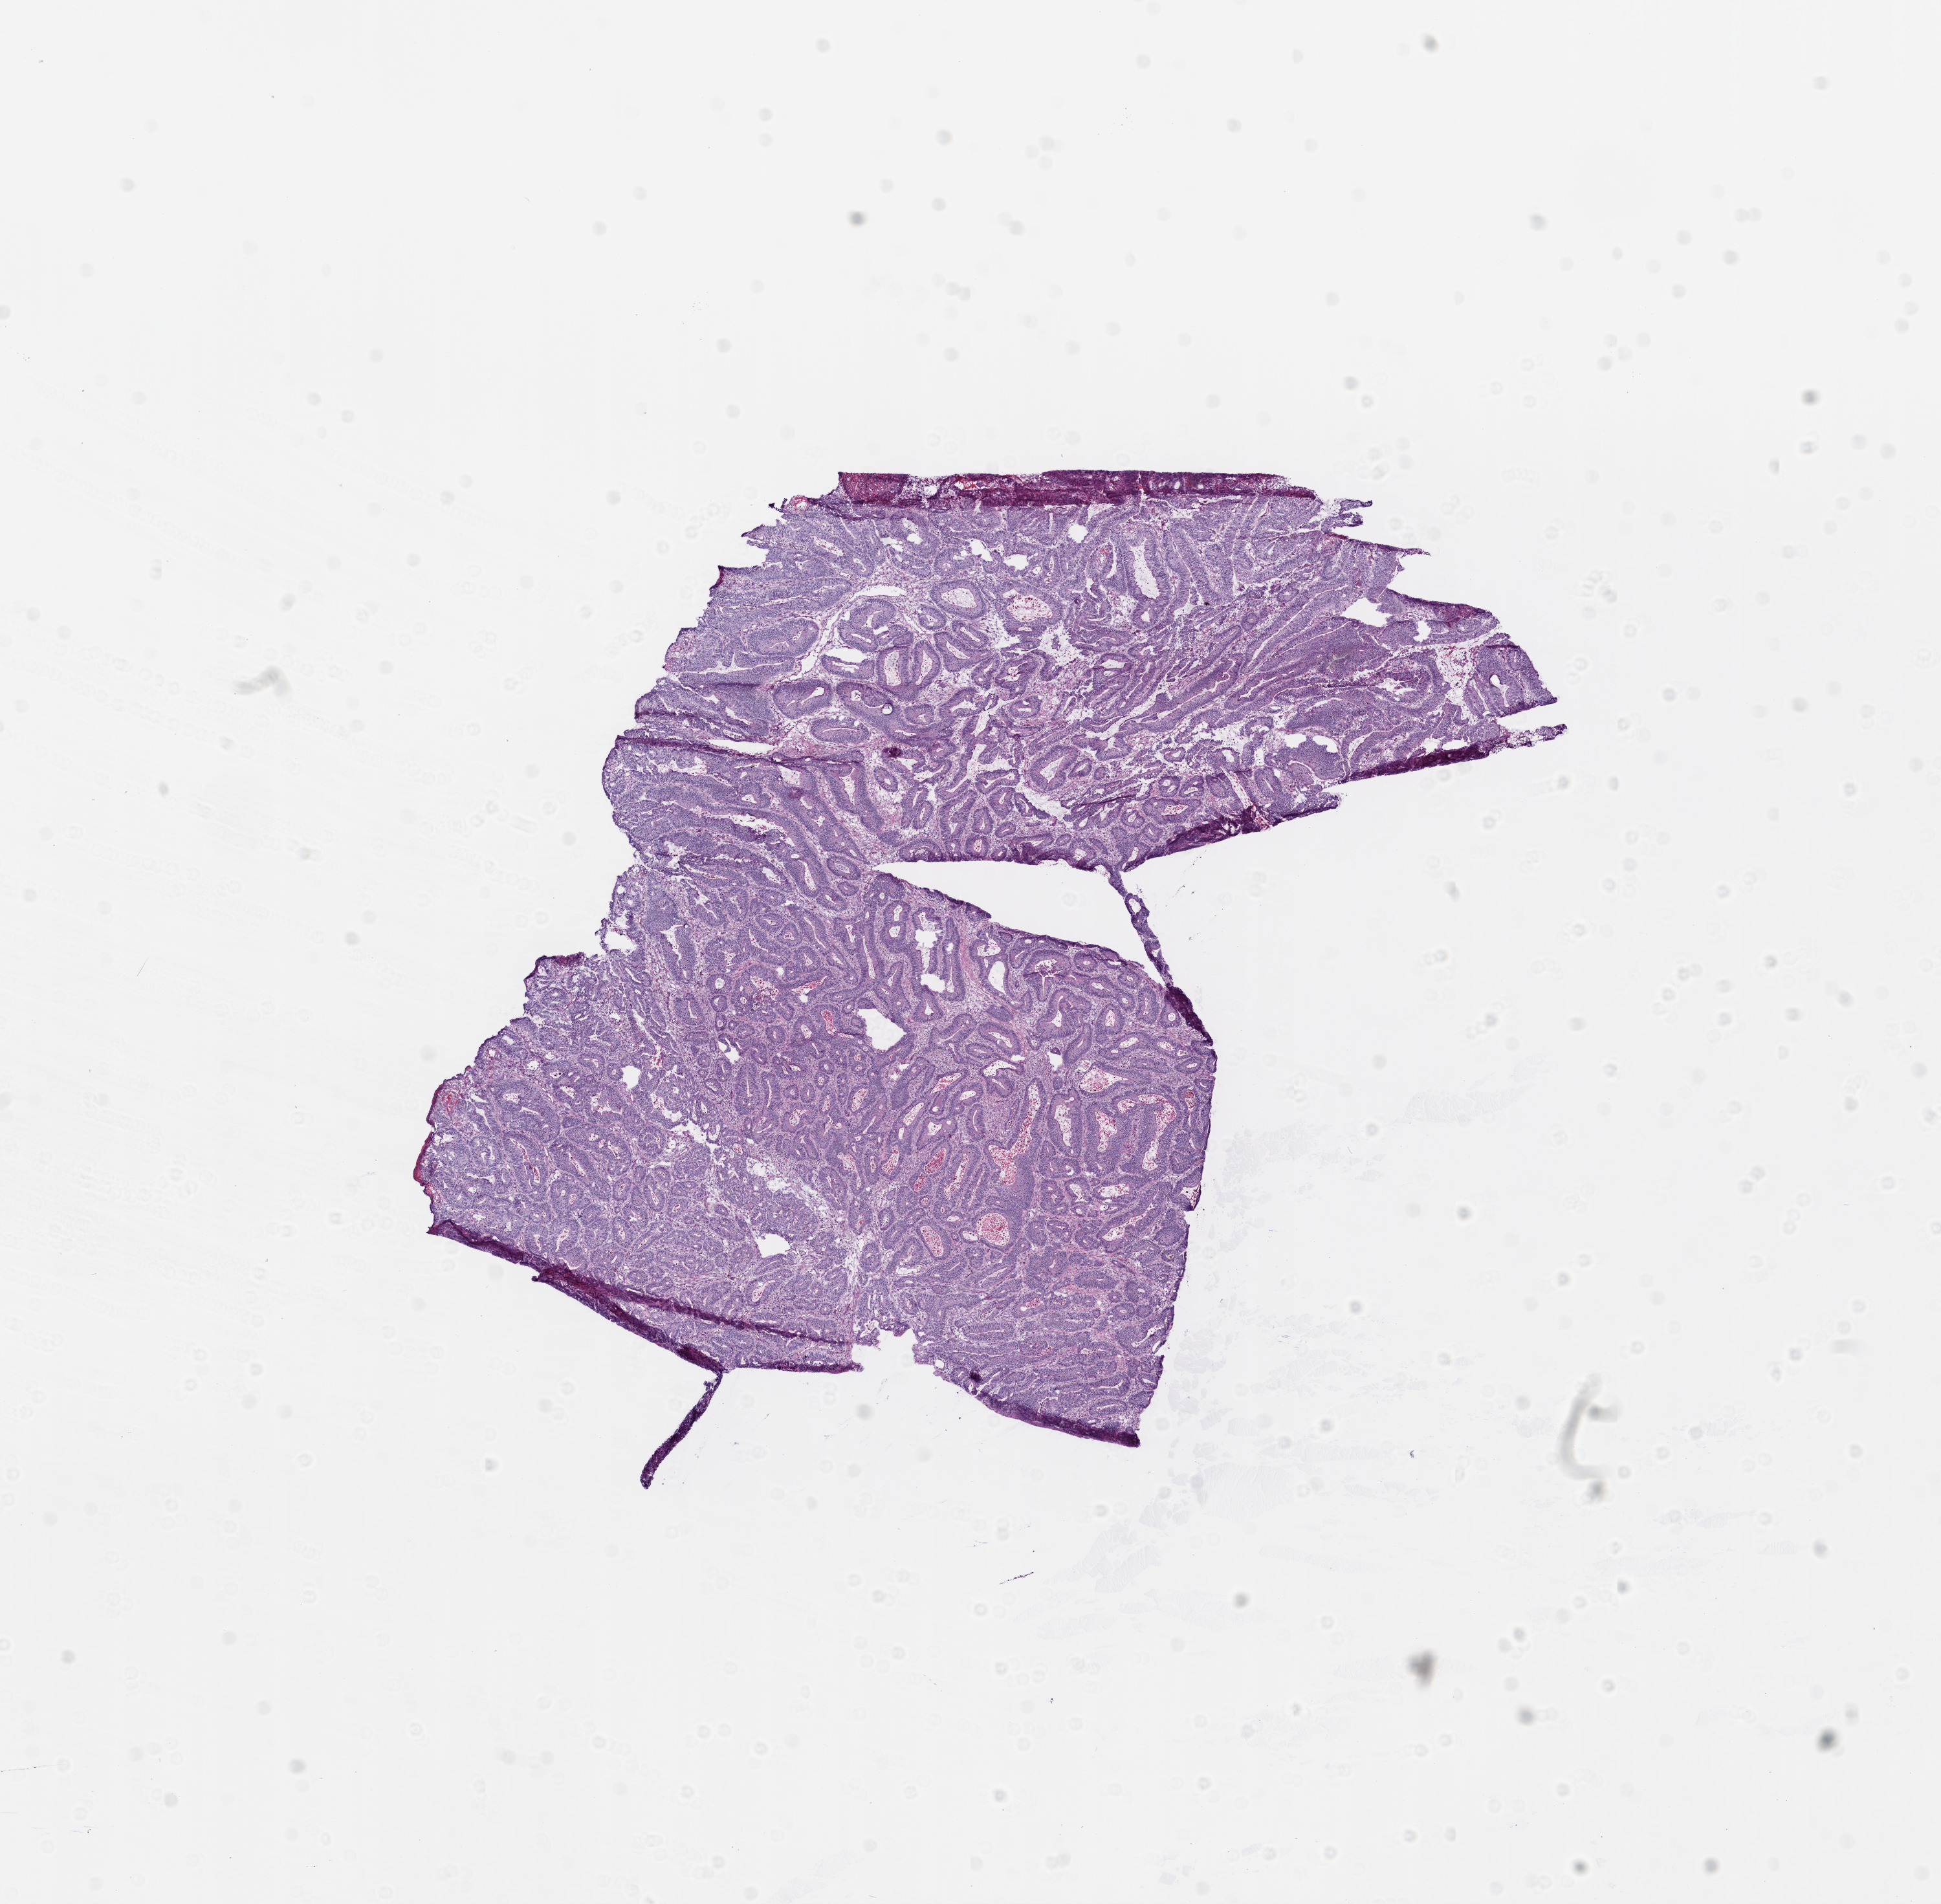
H&E-stained whole-slide image — shown as a low-resolution overview of the whole scanned area (about 12.0 x 11.8 mm). Frozen section from the top of the tissue portion. Colon, primary tumour sample. Patient sex: female. Slide review estimates, as recorded: tumour cells 82%, tumour nuclei 70%, normal cells 0%, stromal cells 10%, necrosis 8%.
AJCC pathologic stage: II. Pathologic diagnosis: Adenocarcinoma, NOS (ascending colon). Lymph nodes positive (case pathology): 0 of 21 examined.